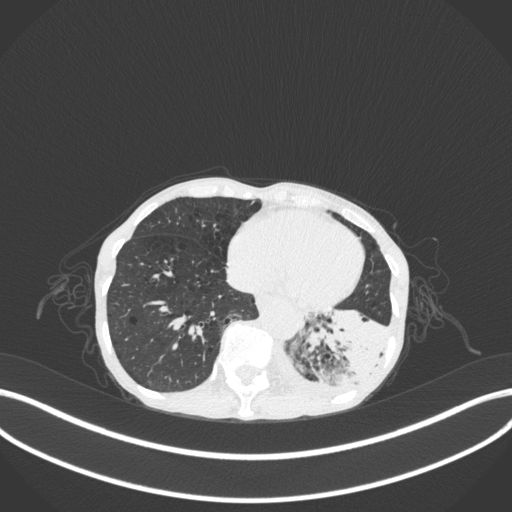
Chest CT, one axial slice; slice 60 of 347 in the series (ordered by position); reconstruction kernel B31f; 120 kVp; lung window (W 1500 / L -600 HU); 512 × 512 image matrix, field of view 400 × 400 mm. Patient: female, 70 years. Case-level facts recorded for this patient, not image findings: clinical TNM (as recorded): T3 N0 M0; histopathological grade: G3.
Outlined on this slice (rectangle marked by the reading radiologist):
- lung tumour (recorded histology: small cell carcinoma): bounding box [x1, y1, x2, y2] px = [296, 297, 392, 395]